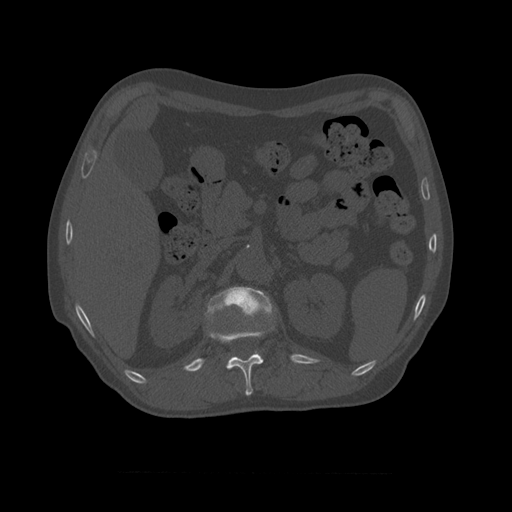
CT including the spine, one axial slice; position 371 of 450 along the scan axis; reconstruction kernel STANDARD; 120 kVp; bone window (W 1800 / L 400 HU); 1.25 mm slice thickness; 512 × 512 image matrix. Patient age 75 years. Case-level facts recorded for this patient, not image findings: primary cancer: prostate.
Annotated regions visible in this slice (semi-automatically segmented with operator editing):
- L1 vertebra: bounding box [x1, y1, x2, y2] px = [205, 287, 273, 332]
- T11 vertebra: [209, 324, 275, 396]